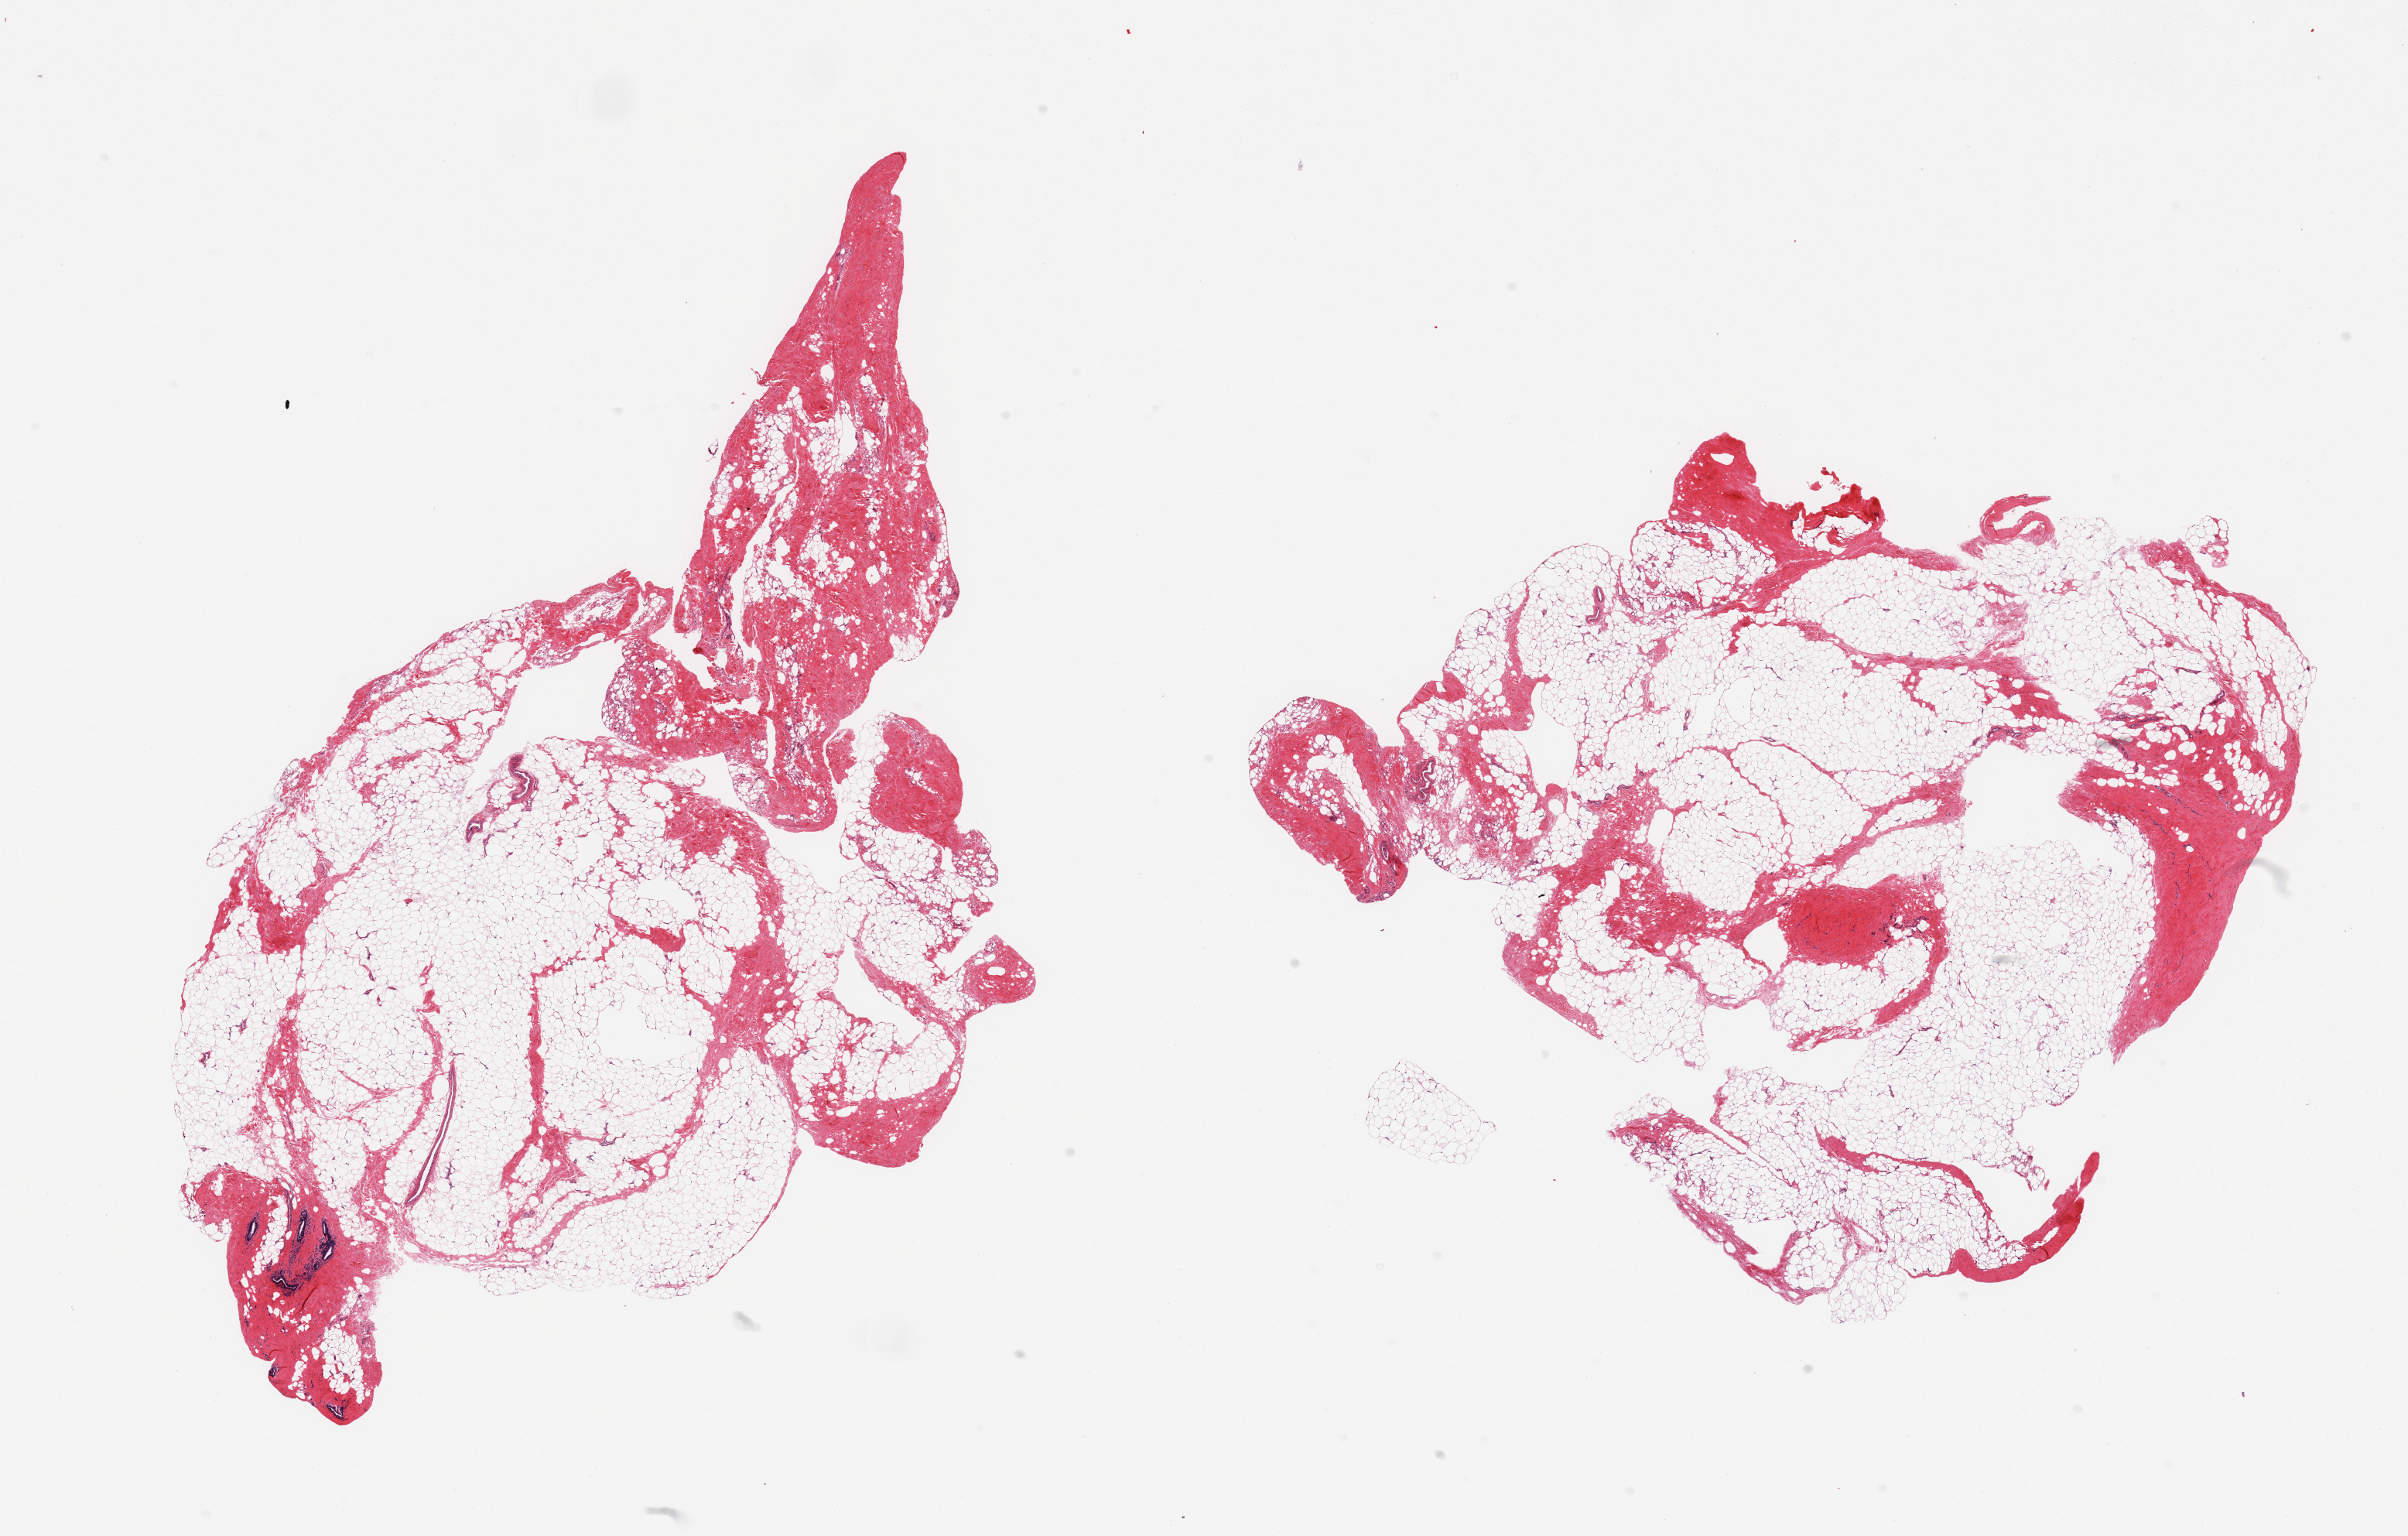
Haematoxylin and eosin whole-slide image — whole scanned area (about 24.6 x 15.7 mm) shown as a low-resolution overview, PAXgene-fixed paraffin-embedded (PFPE) section, section of breast (target tissue), donor tissue sample. Male donor.
* reviewer comment on this tissue sample: 2 pieces; fibrofatty tissue with 1 focus of mammary ducts